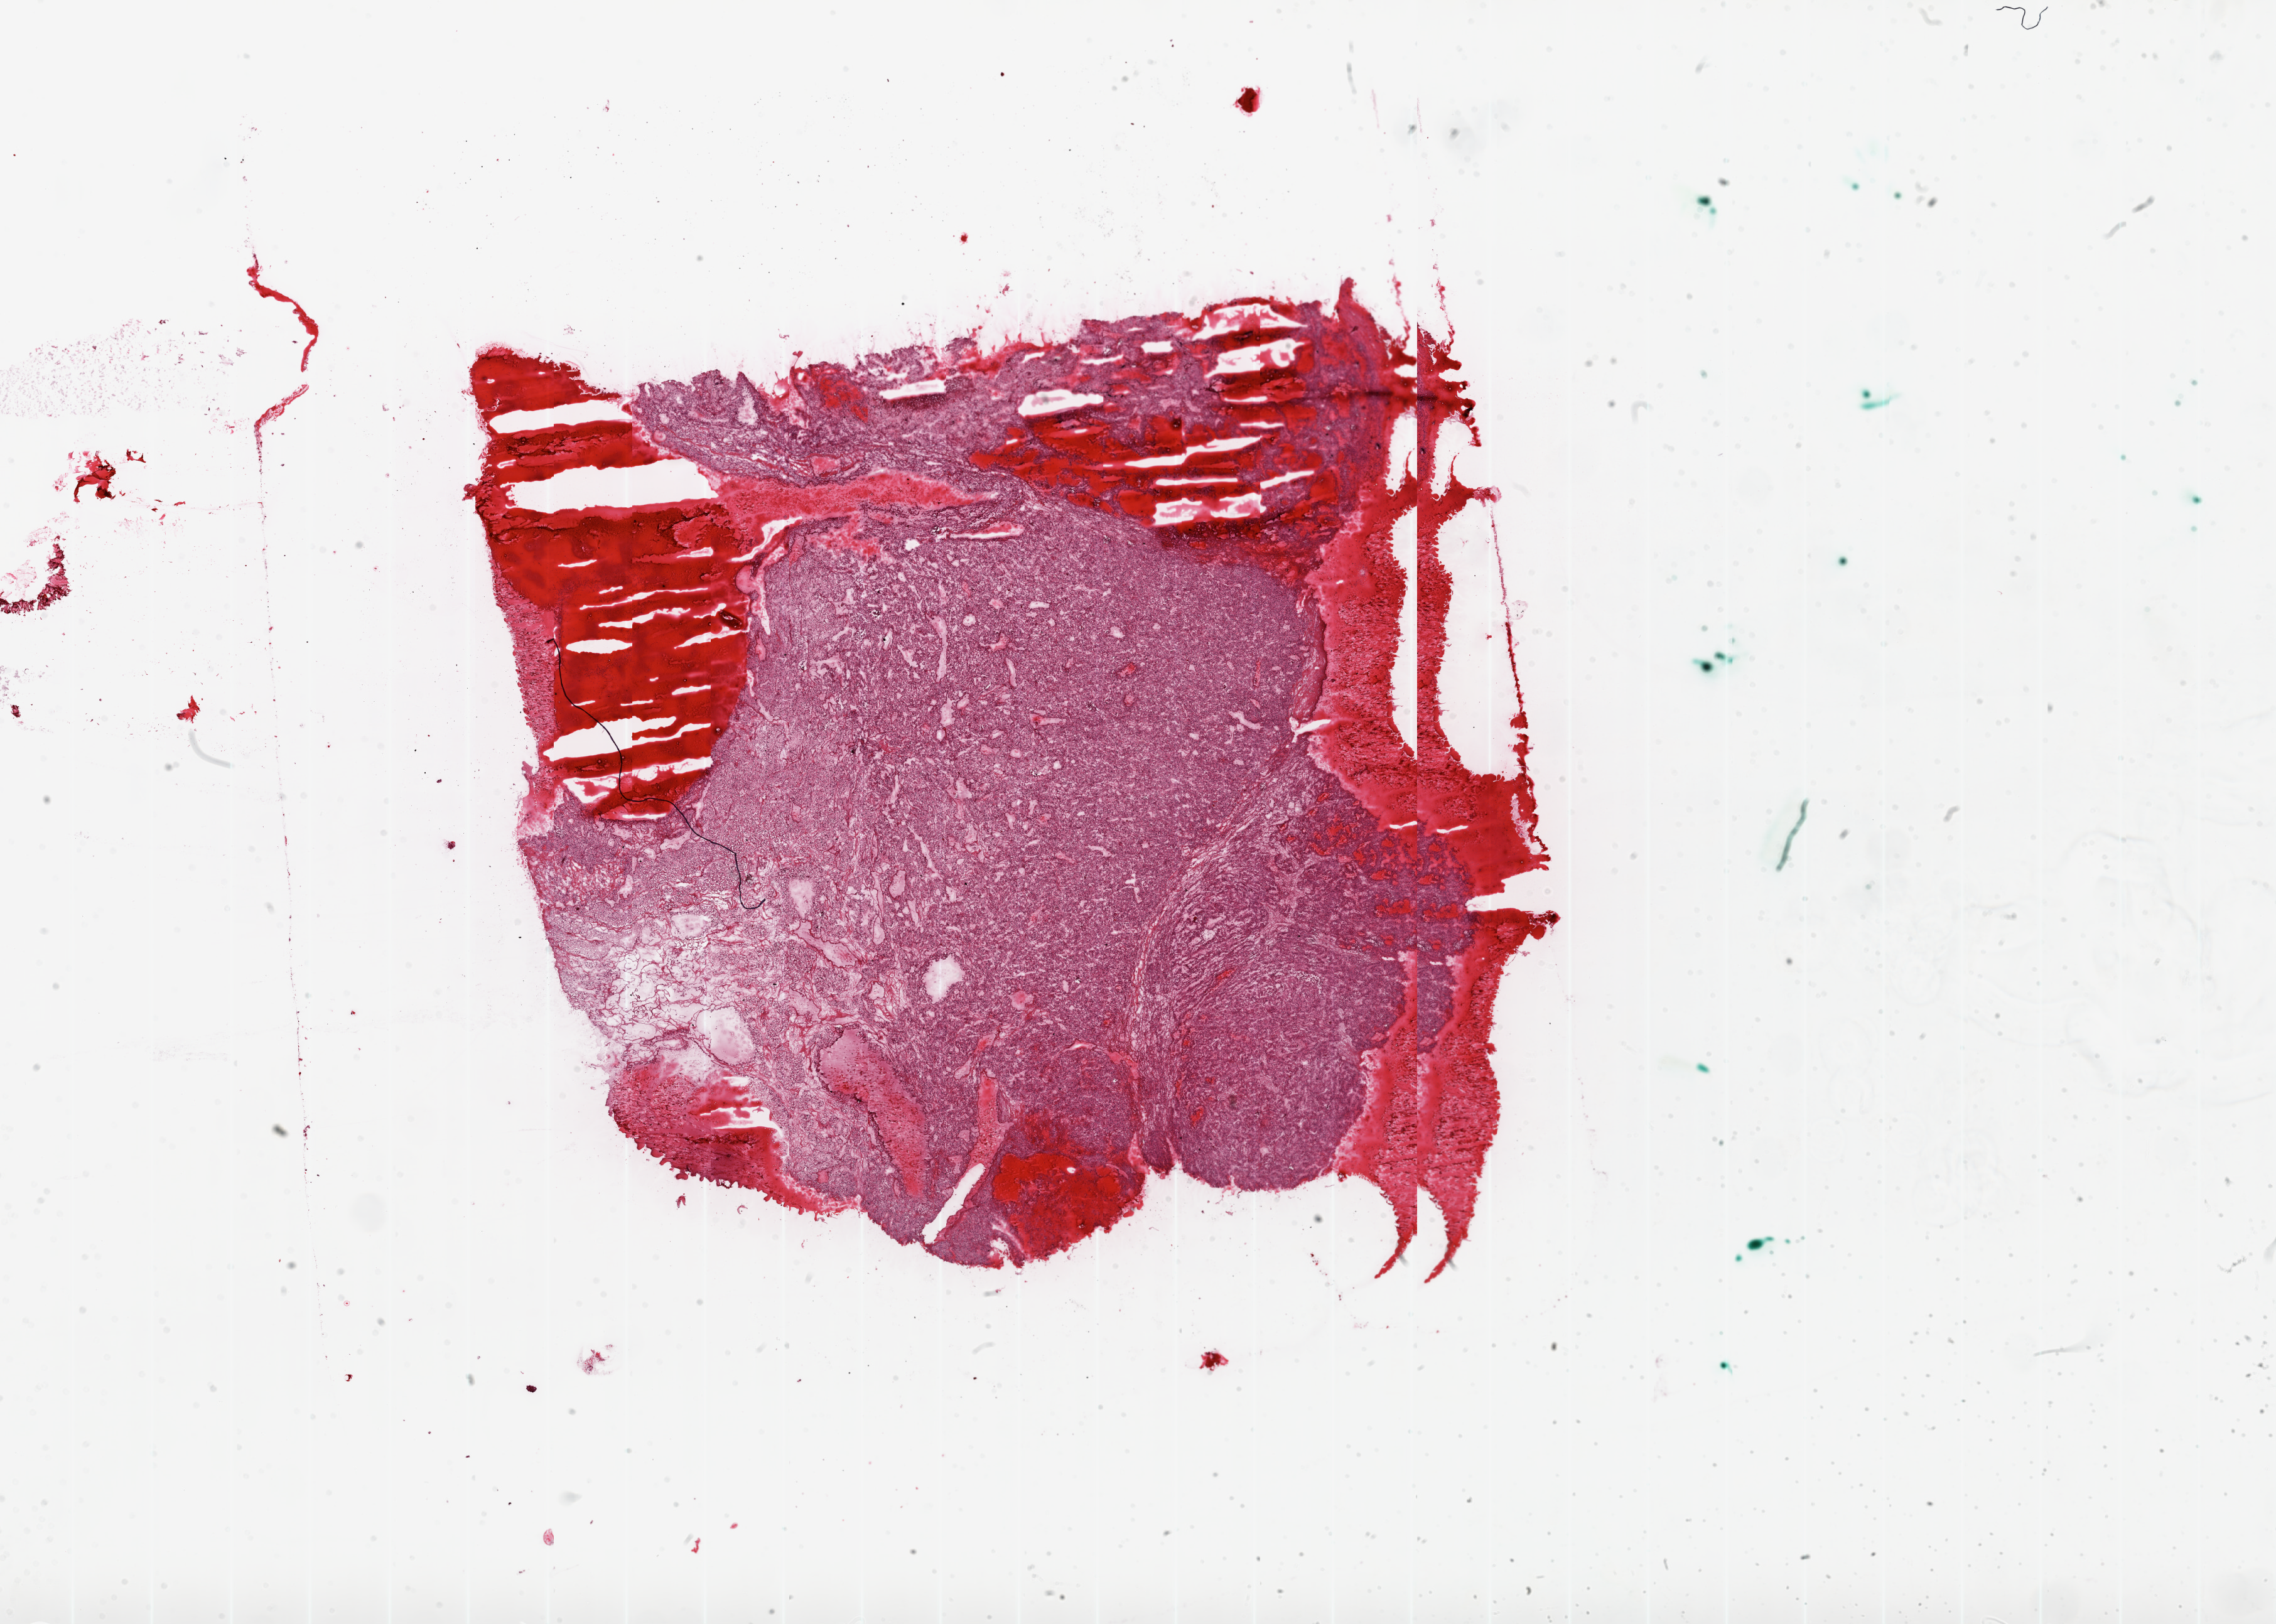
H&E whole-slide image, whole scanned area (about 29.1 x 20.8 mm) shown as a low-resolution overview. Frozen section. Sample: primary tumour, kidney. Male, age 40 years at initial diagnosis. Histologic grade: G3 (poorly differentiated). Slide review estimates, as recorded: tumour cells 85%, tumour nuclei 85%, normal cells 0%, stromal cells 15%, necrosis 0%.
- histologic diagnosis: Clear cell adenocarcinoma, NOS
- AJCC pathologic stage: I